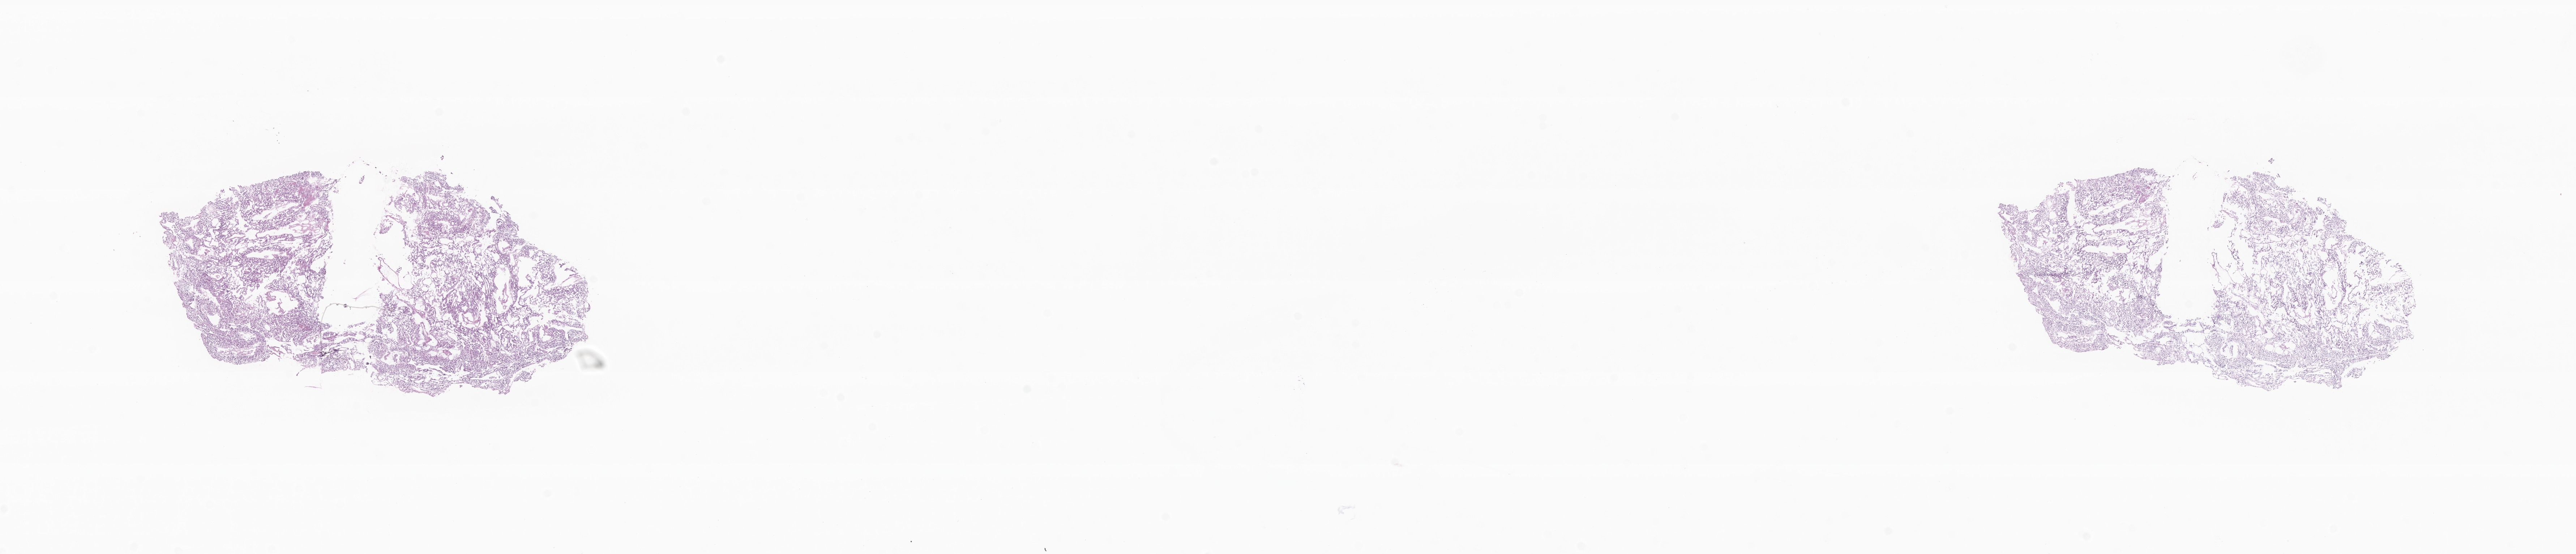
Digitized H&E-stained section of tumor tissue from the spinal cord — whole scanned area (about 30.0 x 6.5 mm) shown as a low-resolution overview. Frozen section. Male patient, age 162 months (13 years 6 months).
Recorded diagnosis: Myxopapillary ependymoma.